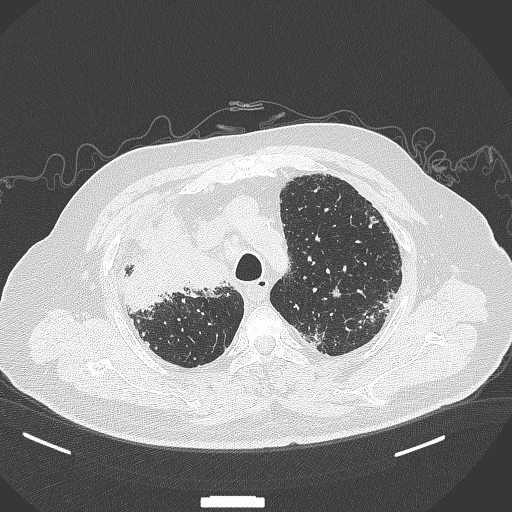
Chest CT, one axial slice; position 284 of 384 along the scan axis; 120 kVp; lung window (W 1500 / L -600 HU); 1 mm slice thickness; 512 × 512 image matrix, field of view 400 × 400 mm. Patient: male, 69 years. Case-level facts recorded for this patient, not image findings: clinical TNM (as recorded): T4 N3 M1.
Outlined on this slice (bounding box drawn by a radiologist):
- lung tumour (recorded histology: adenocarcinoma): bounding box [x1, y1, x2, y2] px = [125, 209, 229, 311]